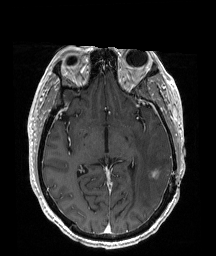
Brain MRI from a brain-tumour surgery series, one axial slice; slice 102 of 192 in the series (ordered by position); T1-weighted post-contrast; 216 × 256 image matrix. From the clinical record (not read from this slice): histopathology: Glioblastoma; WHO grade: 4; IDH mutation: no.
Outlined on this slice (expert manual segmentation):
- tumour: bounding box [x1, y1, x2, y2] px = [144, 167, 151, 175]